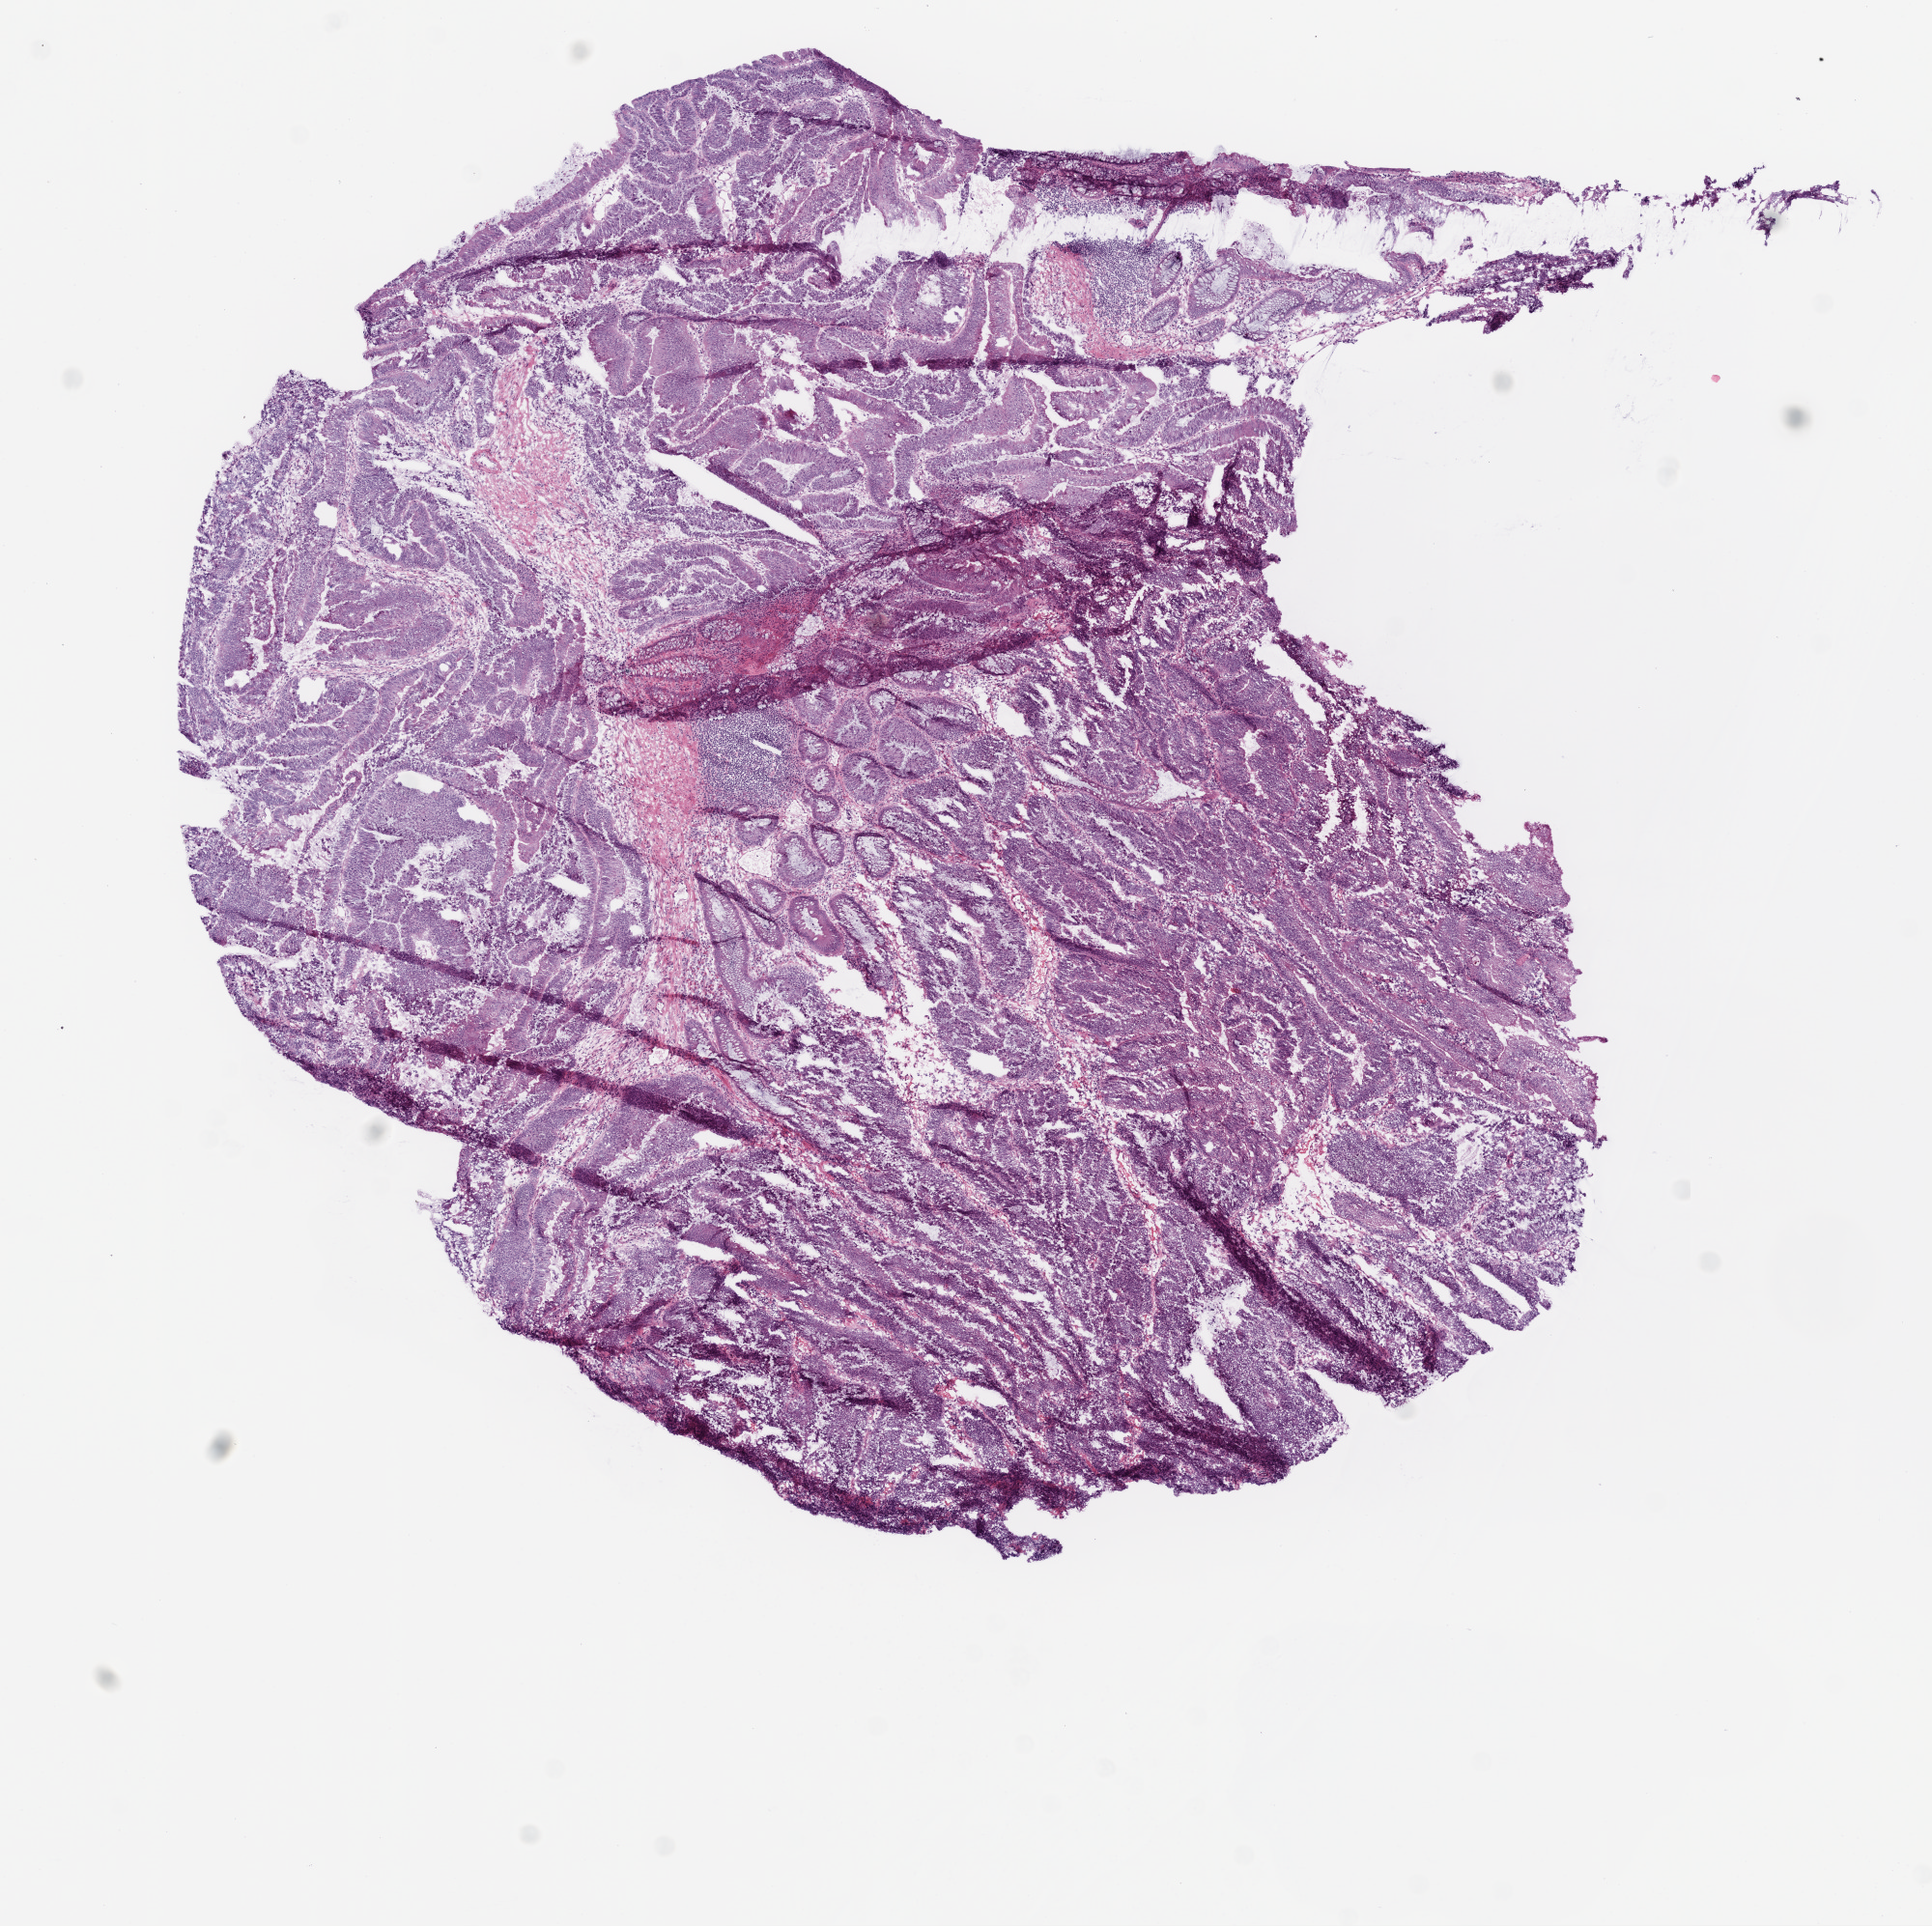
Hematoxylin and eosin (H&E) stained whole-slide image, whole scanned area (about 8.0 x 8.0 mm) shown as a low-resolution overview; frozen section from the top of the tissue portion; rectum, primary tumour sample. Female, age 66 years at initial diagnosis. Composition of this section per pathologist review: tumour cells 80%, tumour nuclei 70%, normal cells 5%, stromal cells 10%, necrosis 5%.
Histologic diagnosis: Adenocarcinoma, NOS (rectosigmoid junction). Lymph nodes positive (case pathology): 0 of 16 examined. AJCC pathologic stage: IIA.